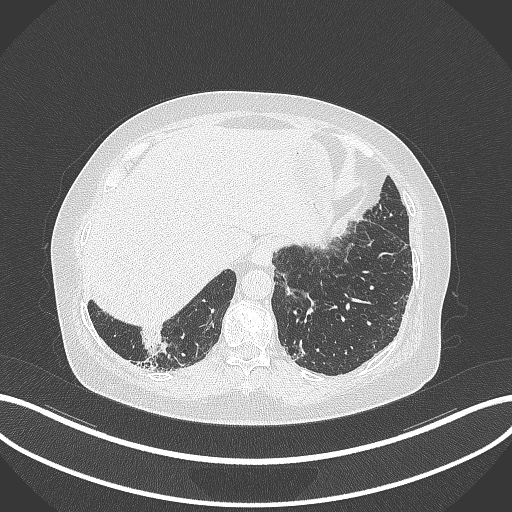
Chest CT, one axial slice; reconstruction kernel B70f; 120 kVp; lung window (W 1500 / L -600 HU); 1 mm slice thickness; 512 × 512 image matrix, field of view 400 × 400 mm. Female patient, age 65 years. Case-level facts recorded for this patient, not image findings: clinical TNM (as recorded): T2b N1 M0.
Outlined on this slice (bounding box drawn by a radiologist):
- lung tumour (recorded histology: adenocarcinoma): box from (x=137, y=328) to (x=169, y=359) px